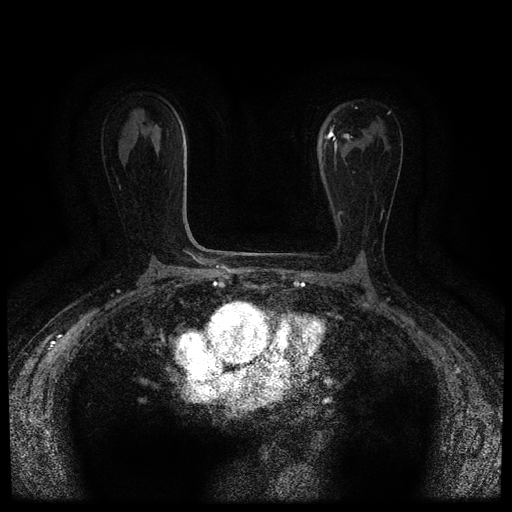
Breast MRI (dynamic contrast-enhanced, multi-phase), one axial slice; slice 48 of 116 in the series (ordered by position); dynamic contrast-enhanced series, time point 2 of 5 at this slice position (early post-contrast); 1.5 T; TE 2.7 ms, TR 5.4 ms; 2 mm slice thickness; 512 × 512 image matrix, field of view 320 × 320 mm. Patient: female, 80 years.
Annotated regions visible in this slice (semi-automatically segmented with operator editing):
- breast lesion (labelled 'tumour' in the annotation; benign lesions carry a separate 'benign' label): bounding box (x1, y1, x2, y2) in pixels: (343, 133, 353, 141)